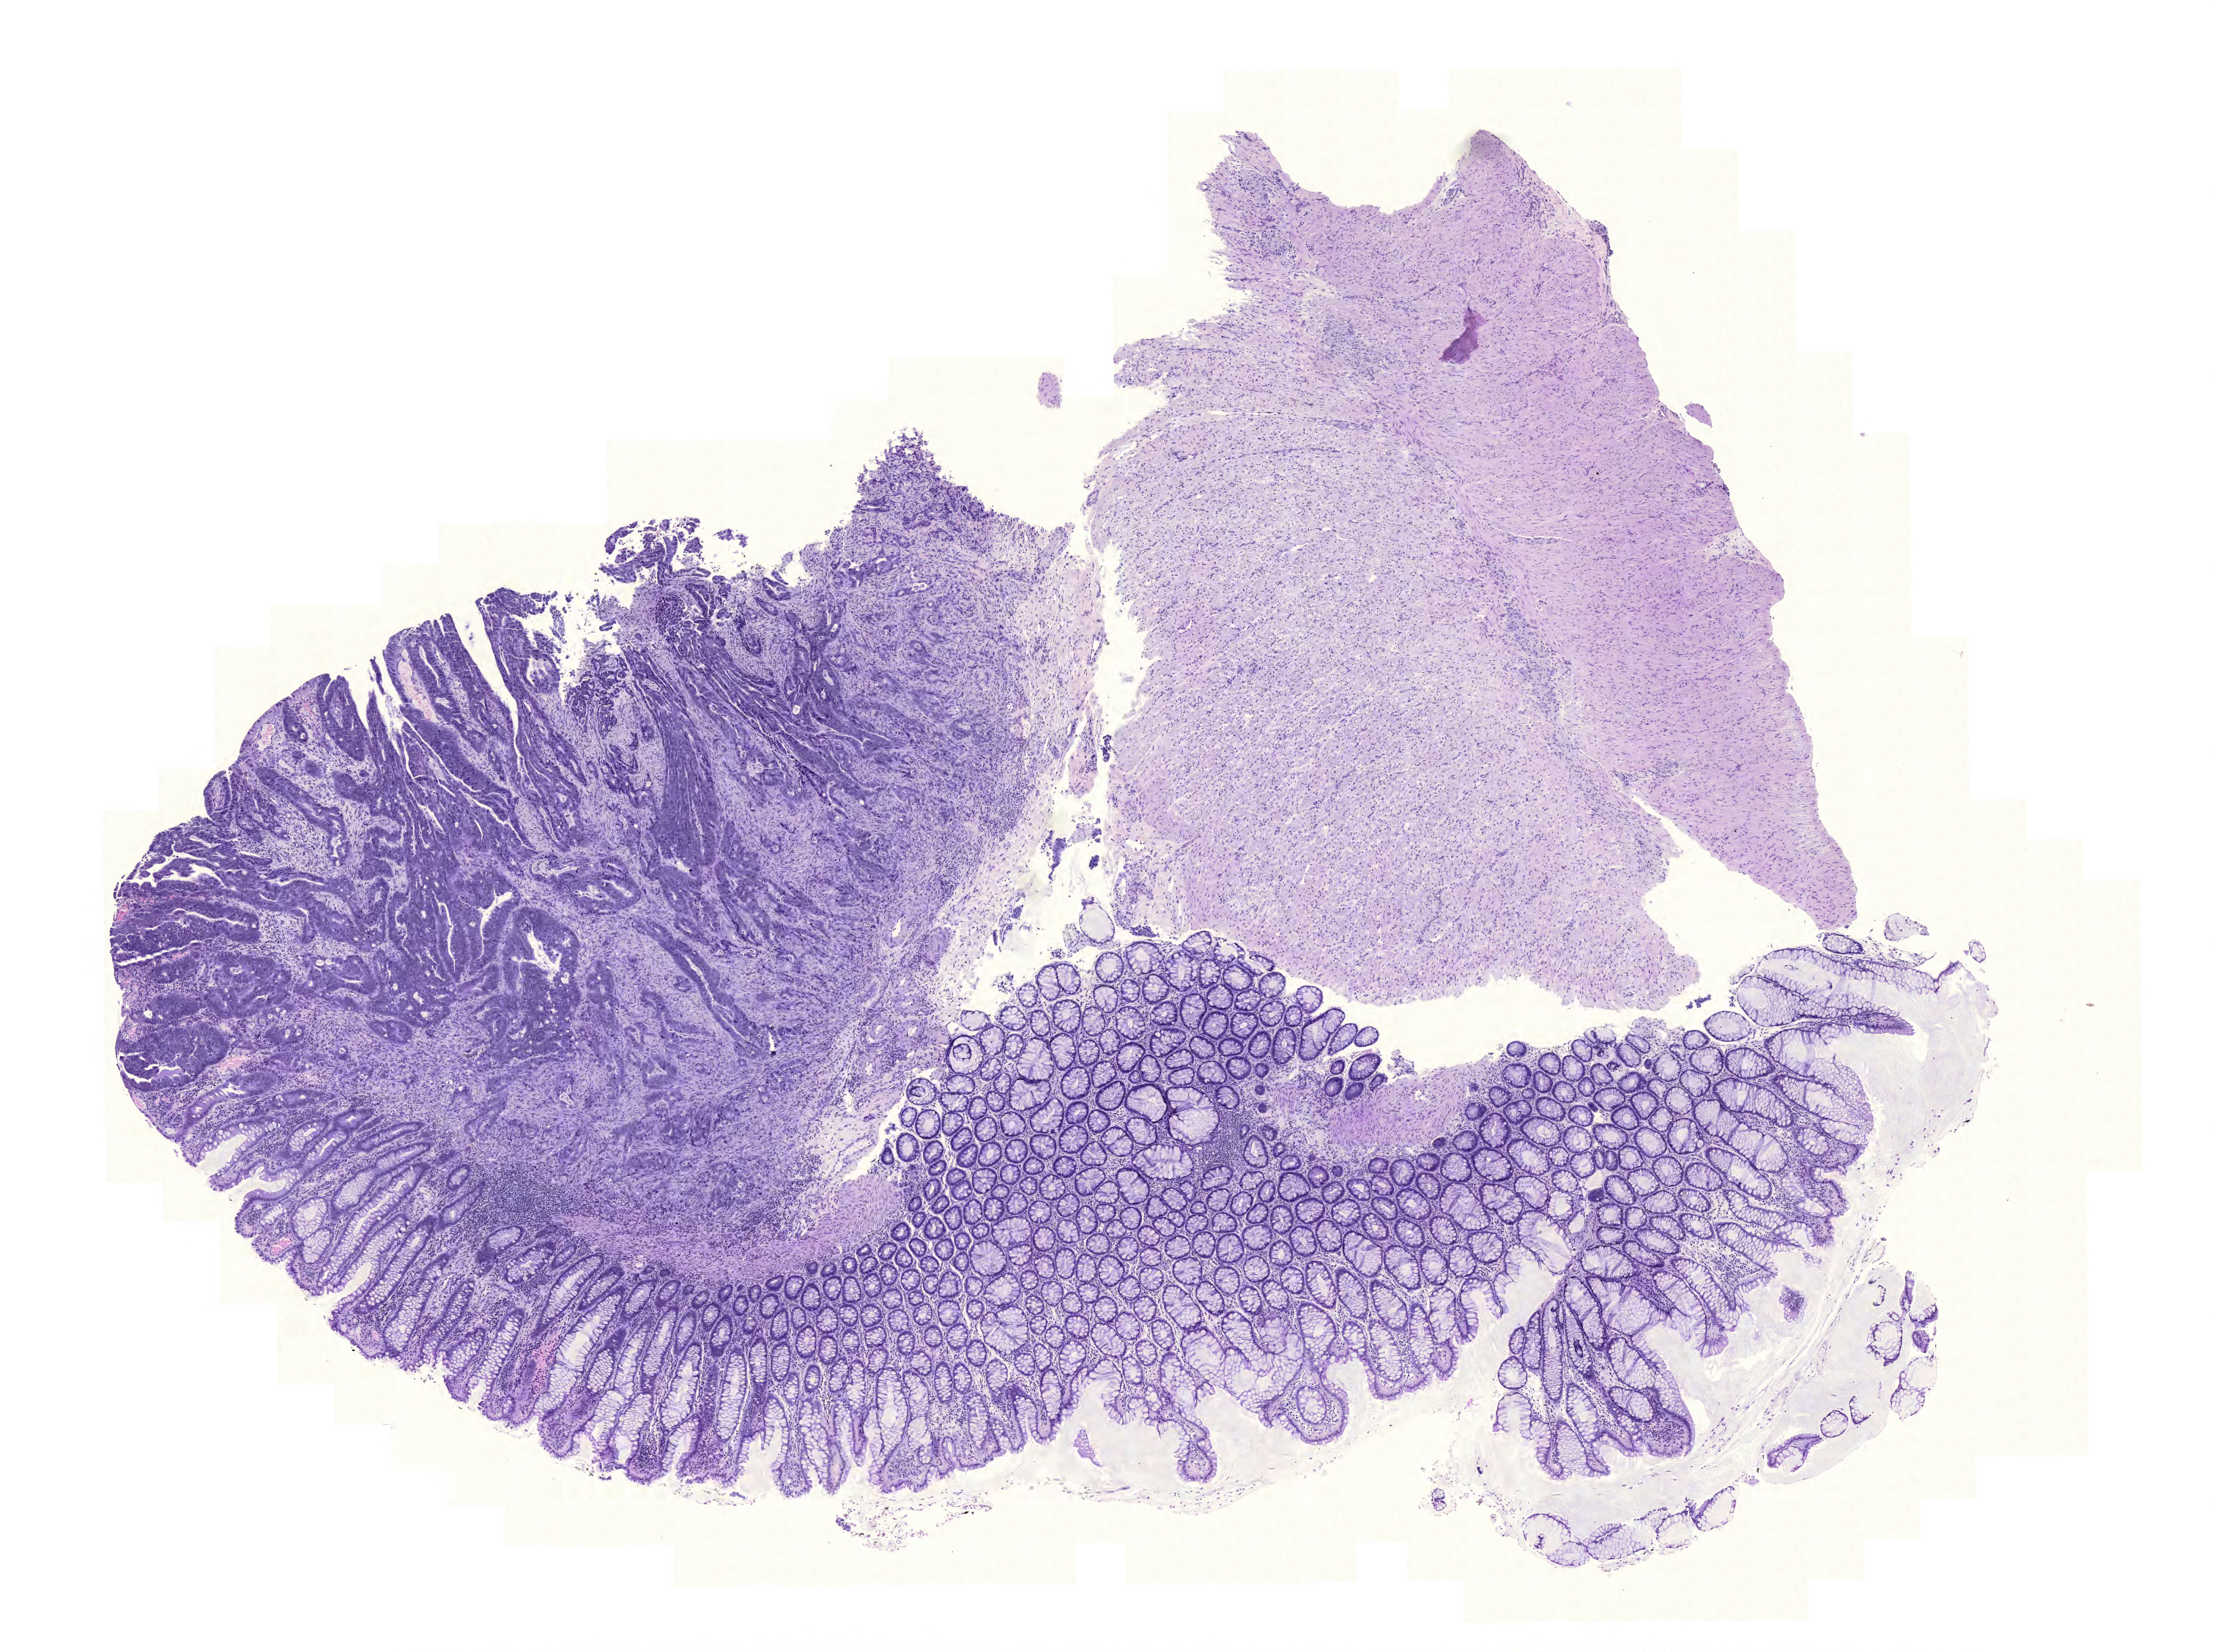
H&E-stained whole-slide image — a low-resolution overview of the entire scanned area, about 11.2 x 8.4 mm. Formalin-fixed paraffin-embedded (FFPE) diagnostic section. Primary tumour sample from the rectum. Patient: male, age at initial diagnosis 64 years.
- AJCC pathologic stage: IV (6th edition)
- histologic diagnosis: Adenocarcinoma, NOS
- lymph nodes positive (case pathology): 7 of 40 examined